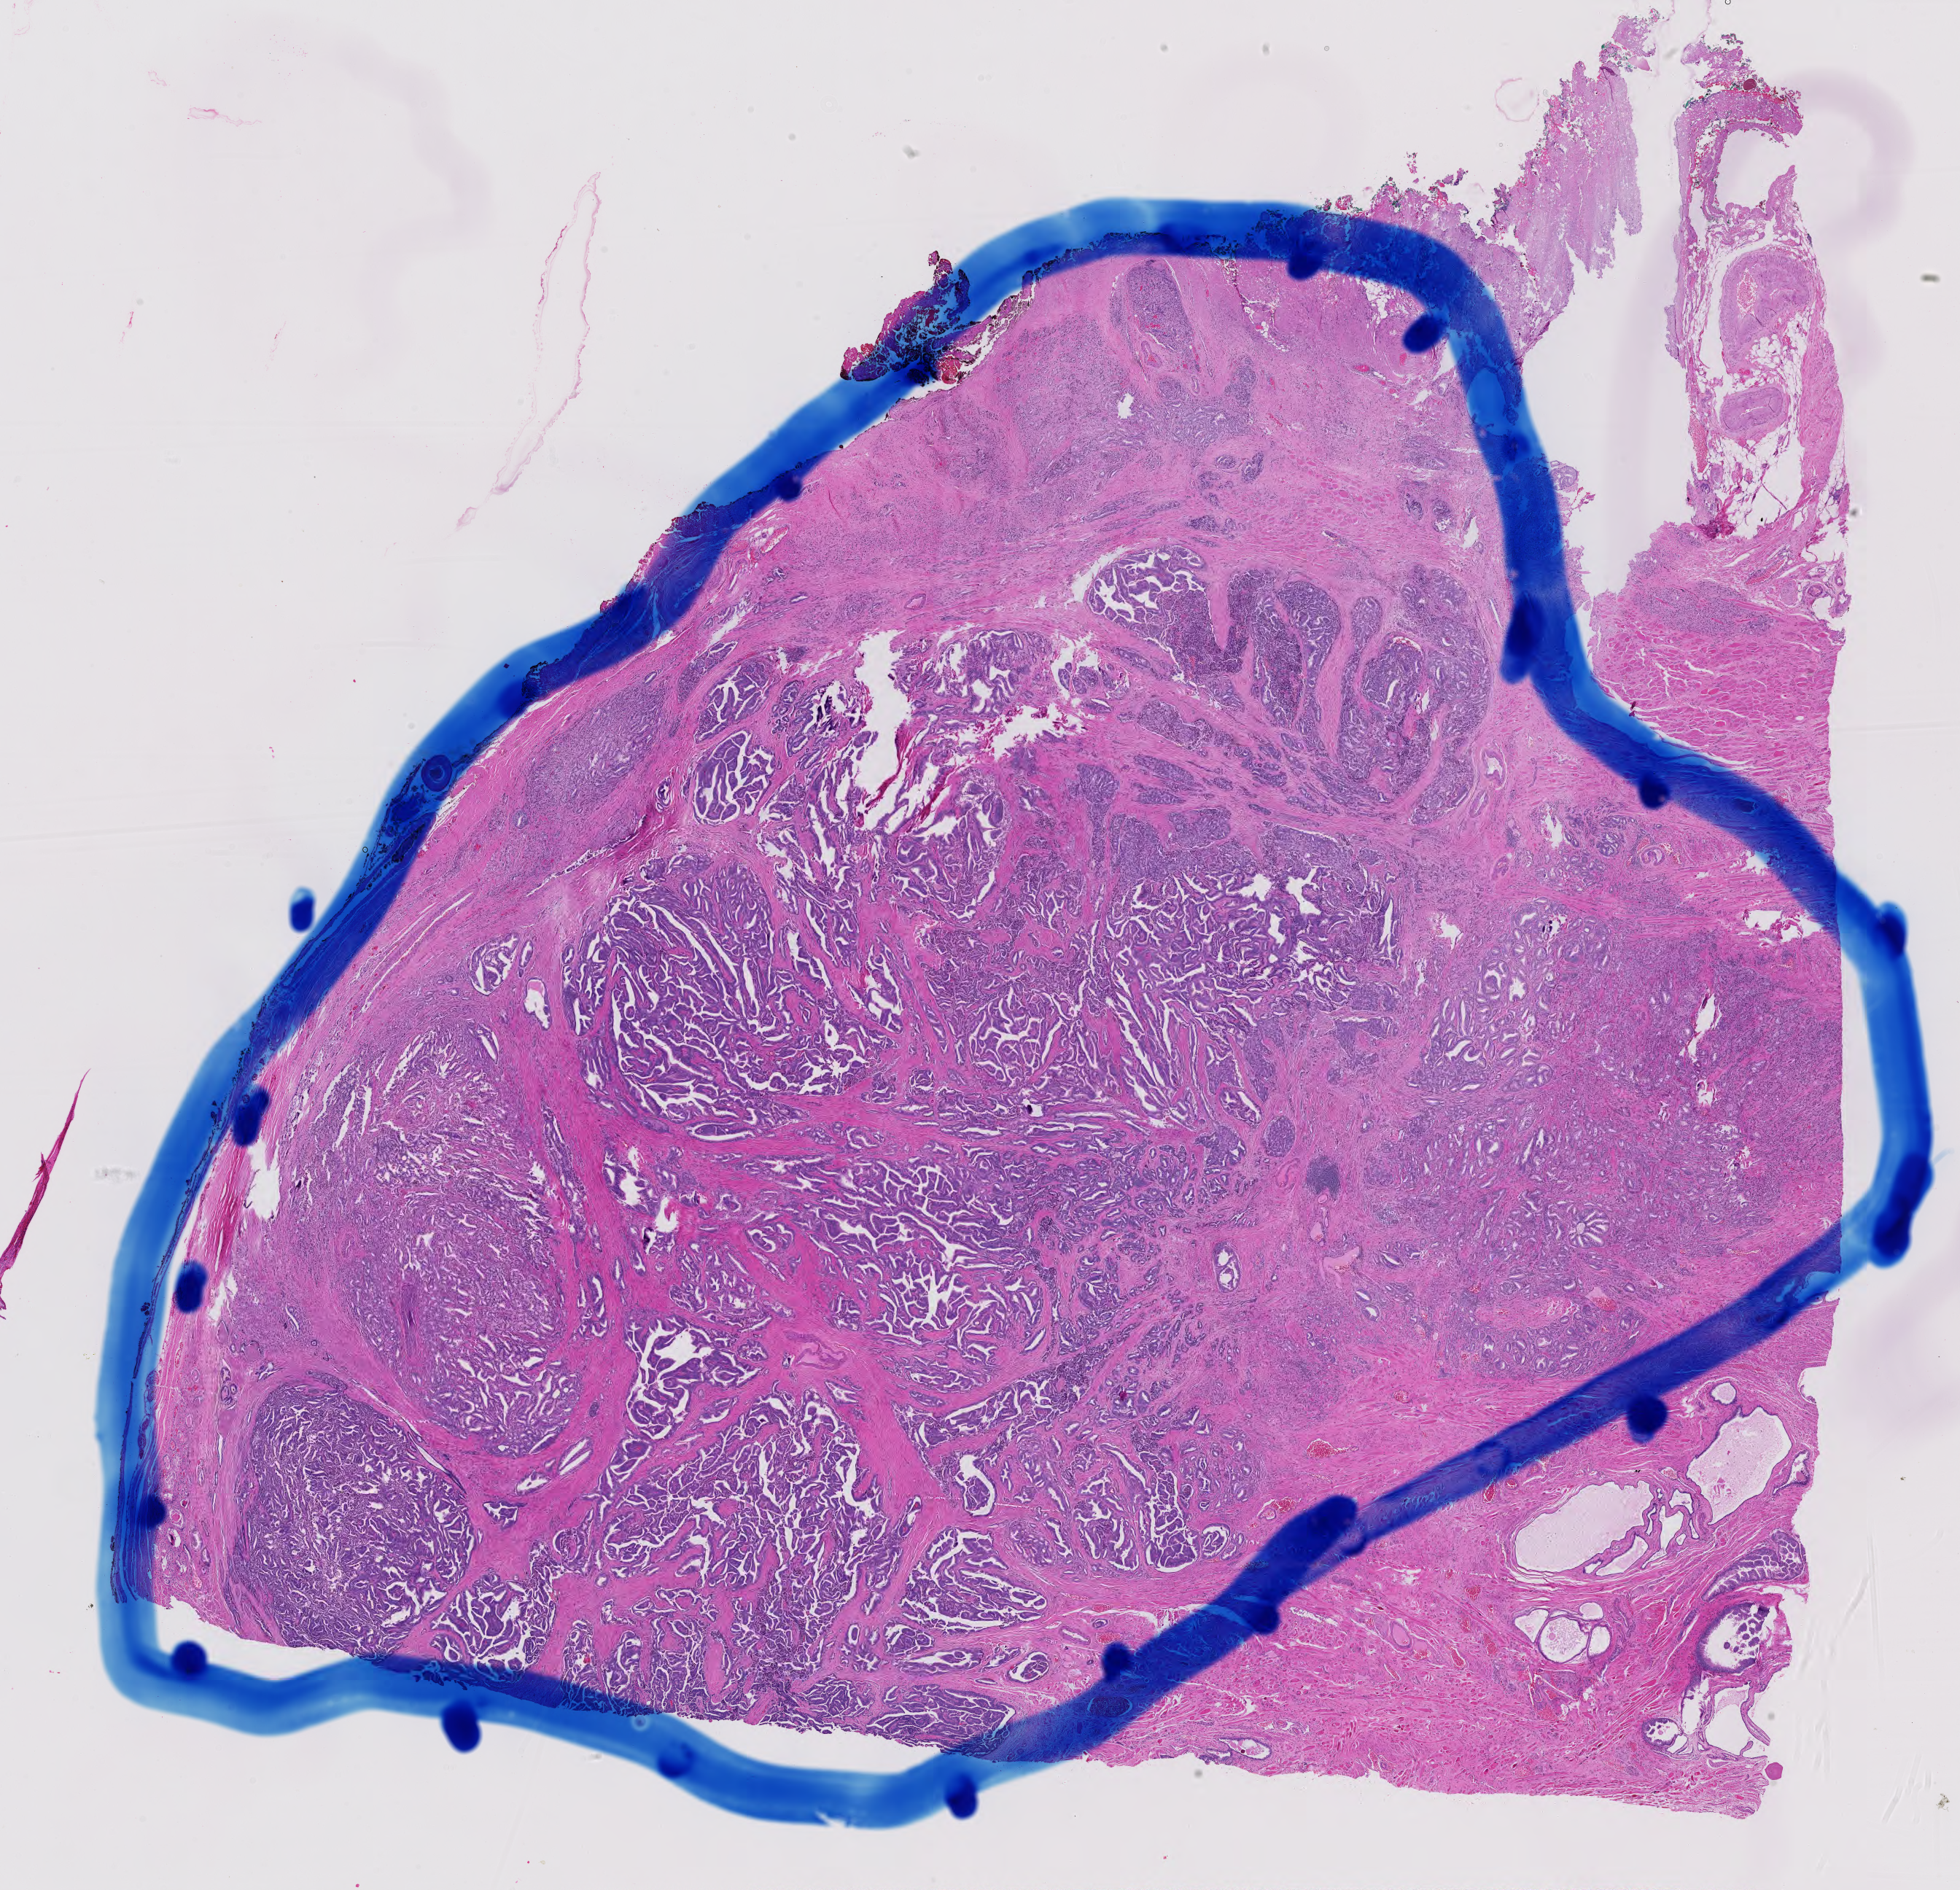
Whole-slide histology image, H&E, shown as a low-resolution overview of the whole scanned area (about 19.5 x 18.8 mm, from a 40x scan); formalin-fixed paraffin-embedded (FFPE) diagnostic section; prostate, primary tumour sample. Male, age 63 years at initial diagnosis. Gleason score: 9 (4+5).
Laterality: bilateral. Histologic diagnosis: Adenocarcinoma, NOS (prostate gland).